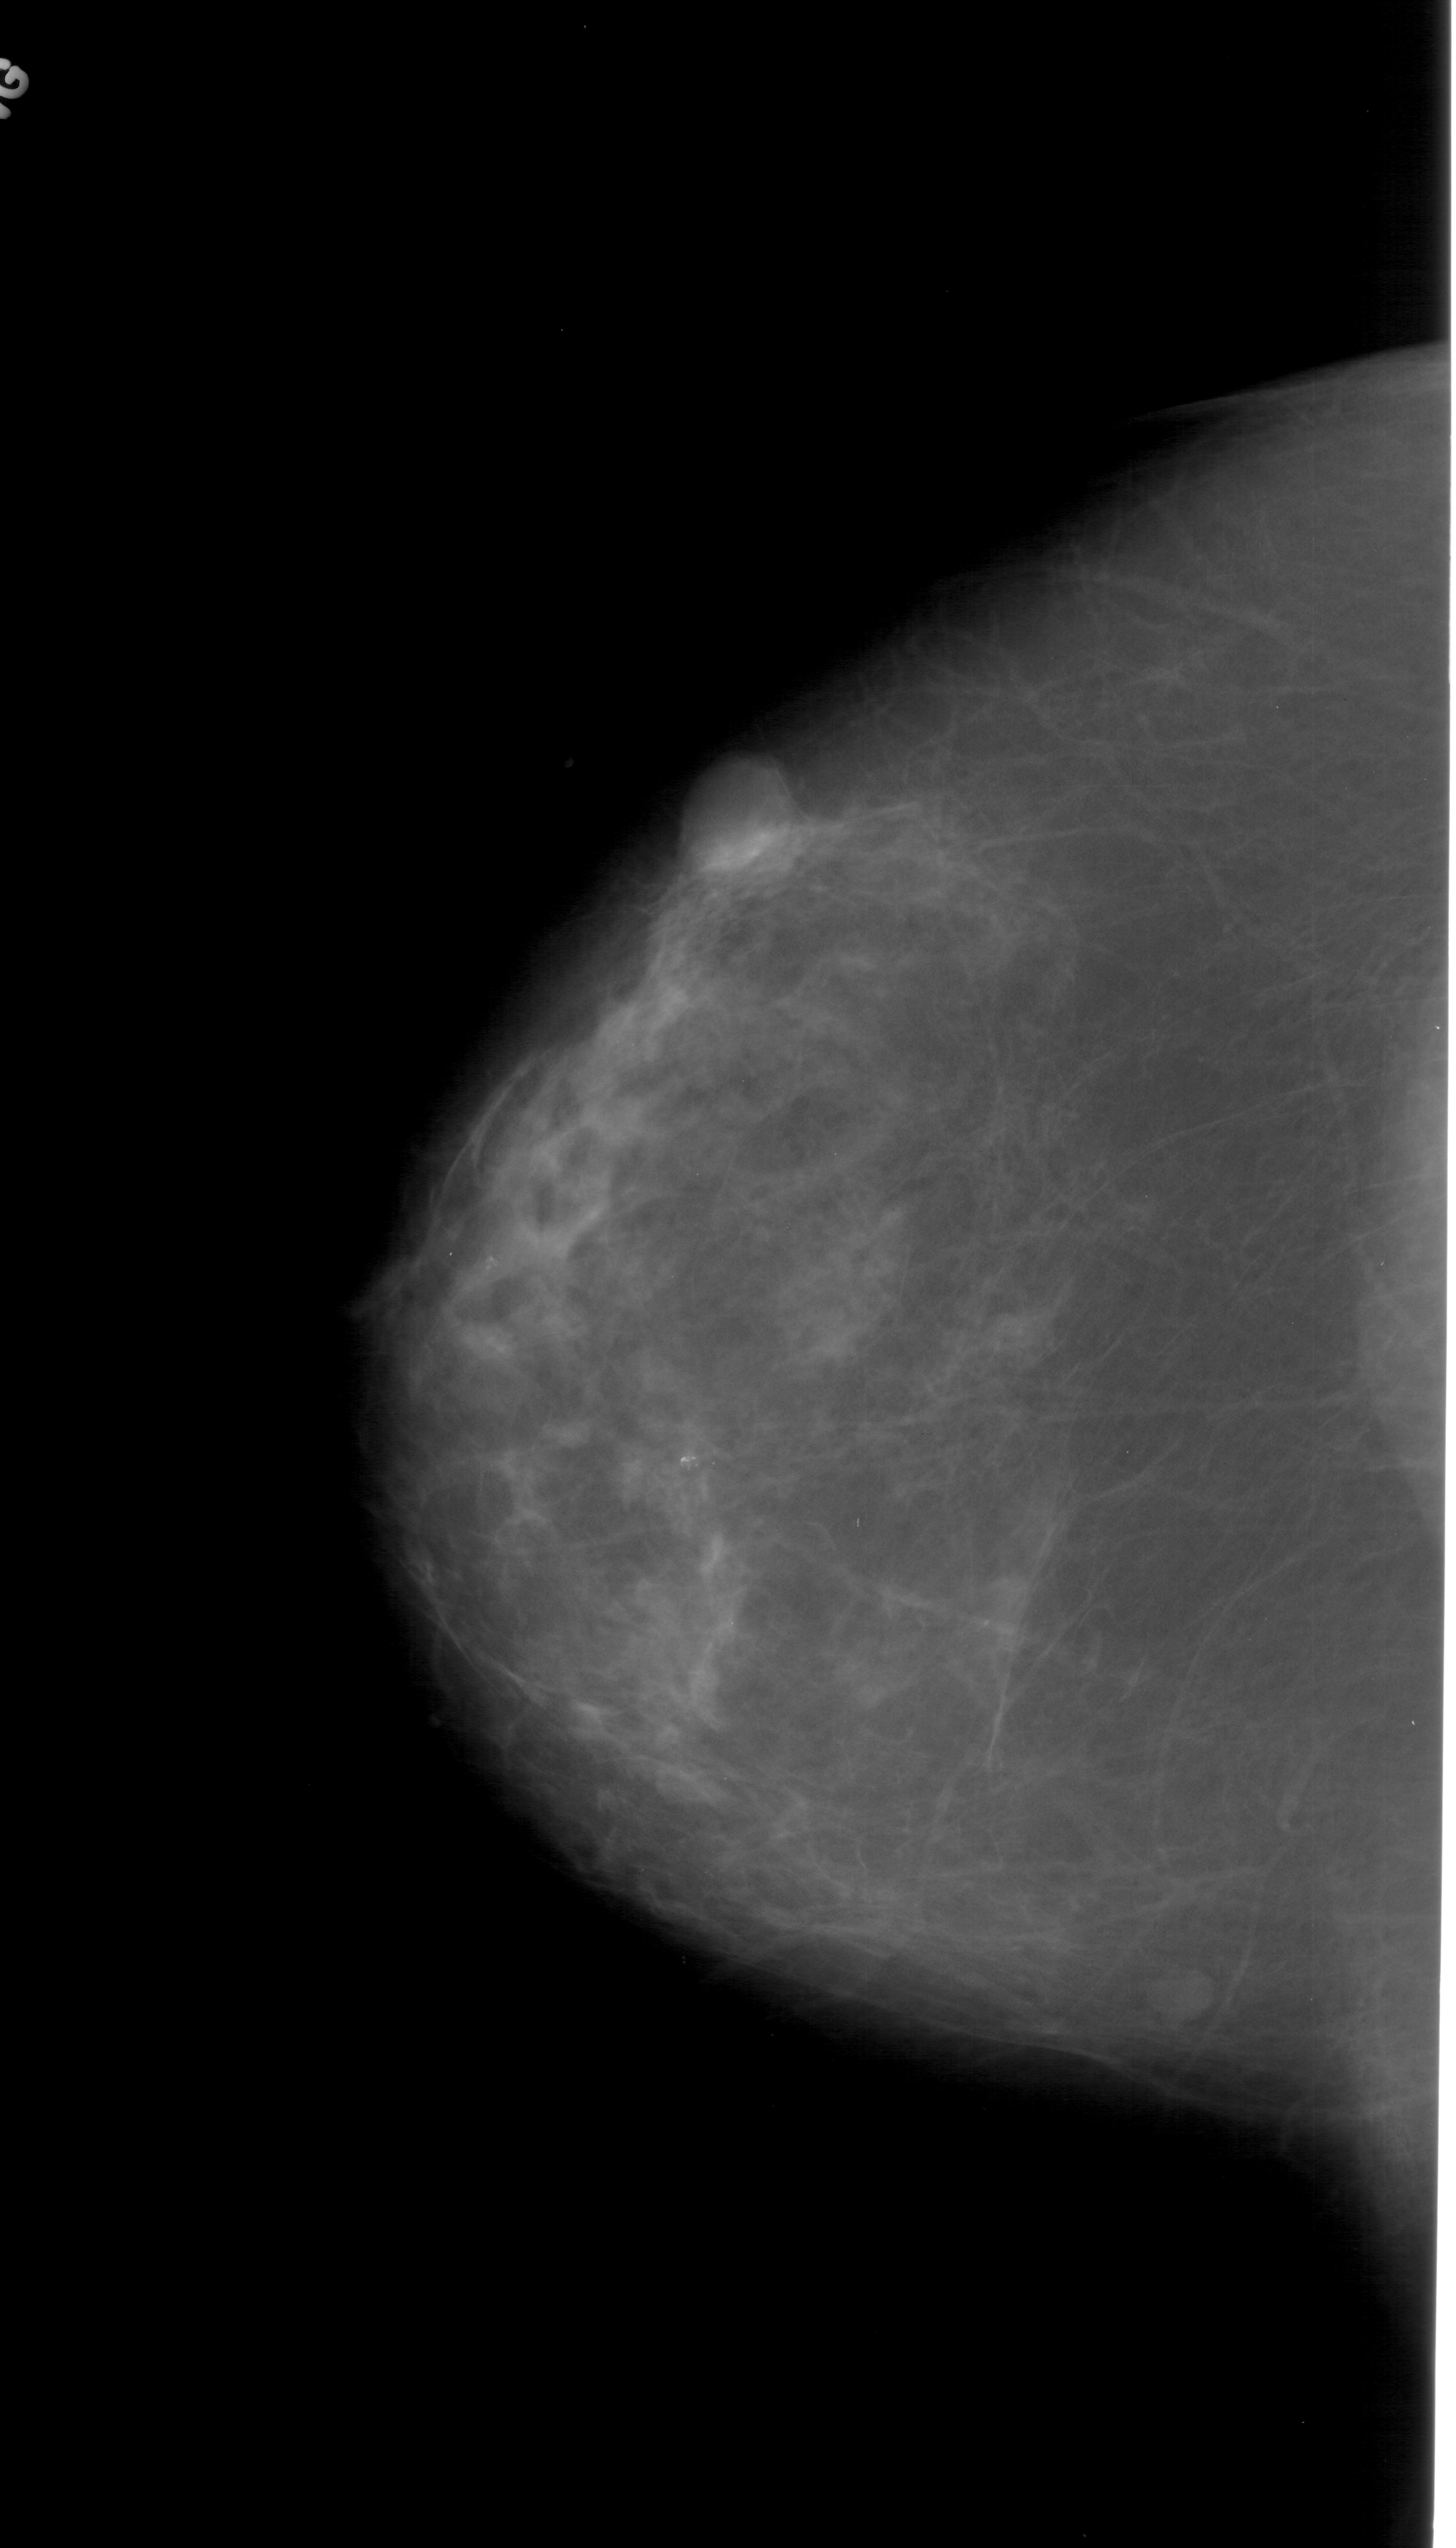
Digitized screen-film mammogram; left breast; craniocaudal (CC) view; breast composition: scattered fibroglandular densities (BI-RADS density category 2 of 4).
Marked findings (only marked abnormalities are described; nothing is implied about the rest of the image): mass, shape lobulated, margins circumscribed; BI-RADS assessment category 4; pathology (as recorded): benign.